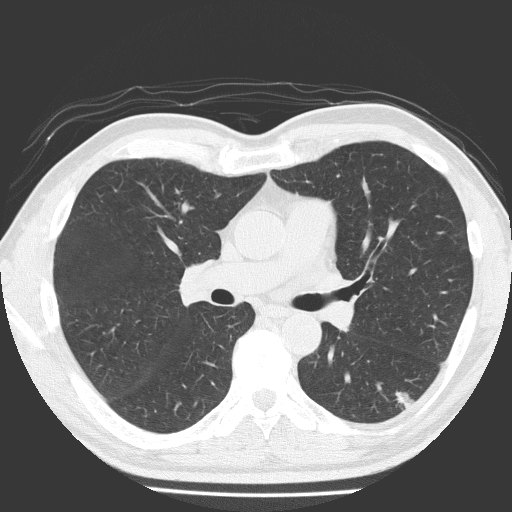
Low-dose screening chest CT, one axial slice. Position 106 of 184 along the scan axis. Lung window (W 1500 / L -600 HU). 2 mm slice thickness. 512 × 512 image matrix.
Outlined on this slice (manually delineated by an expert):
- lesion 1 (tumor, lower lobe of left lung): bounding box (x1, y1, x2, y2) in pixels: (395, 391, 415, 410)